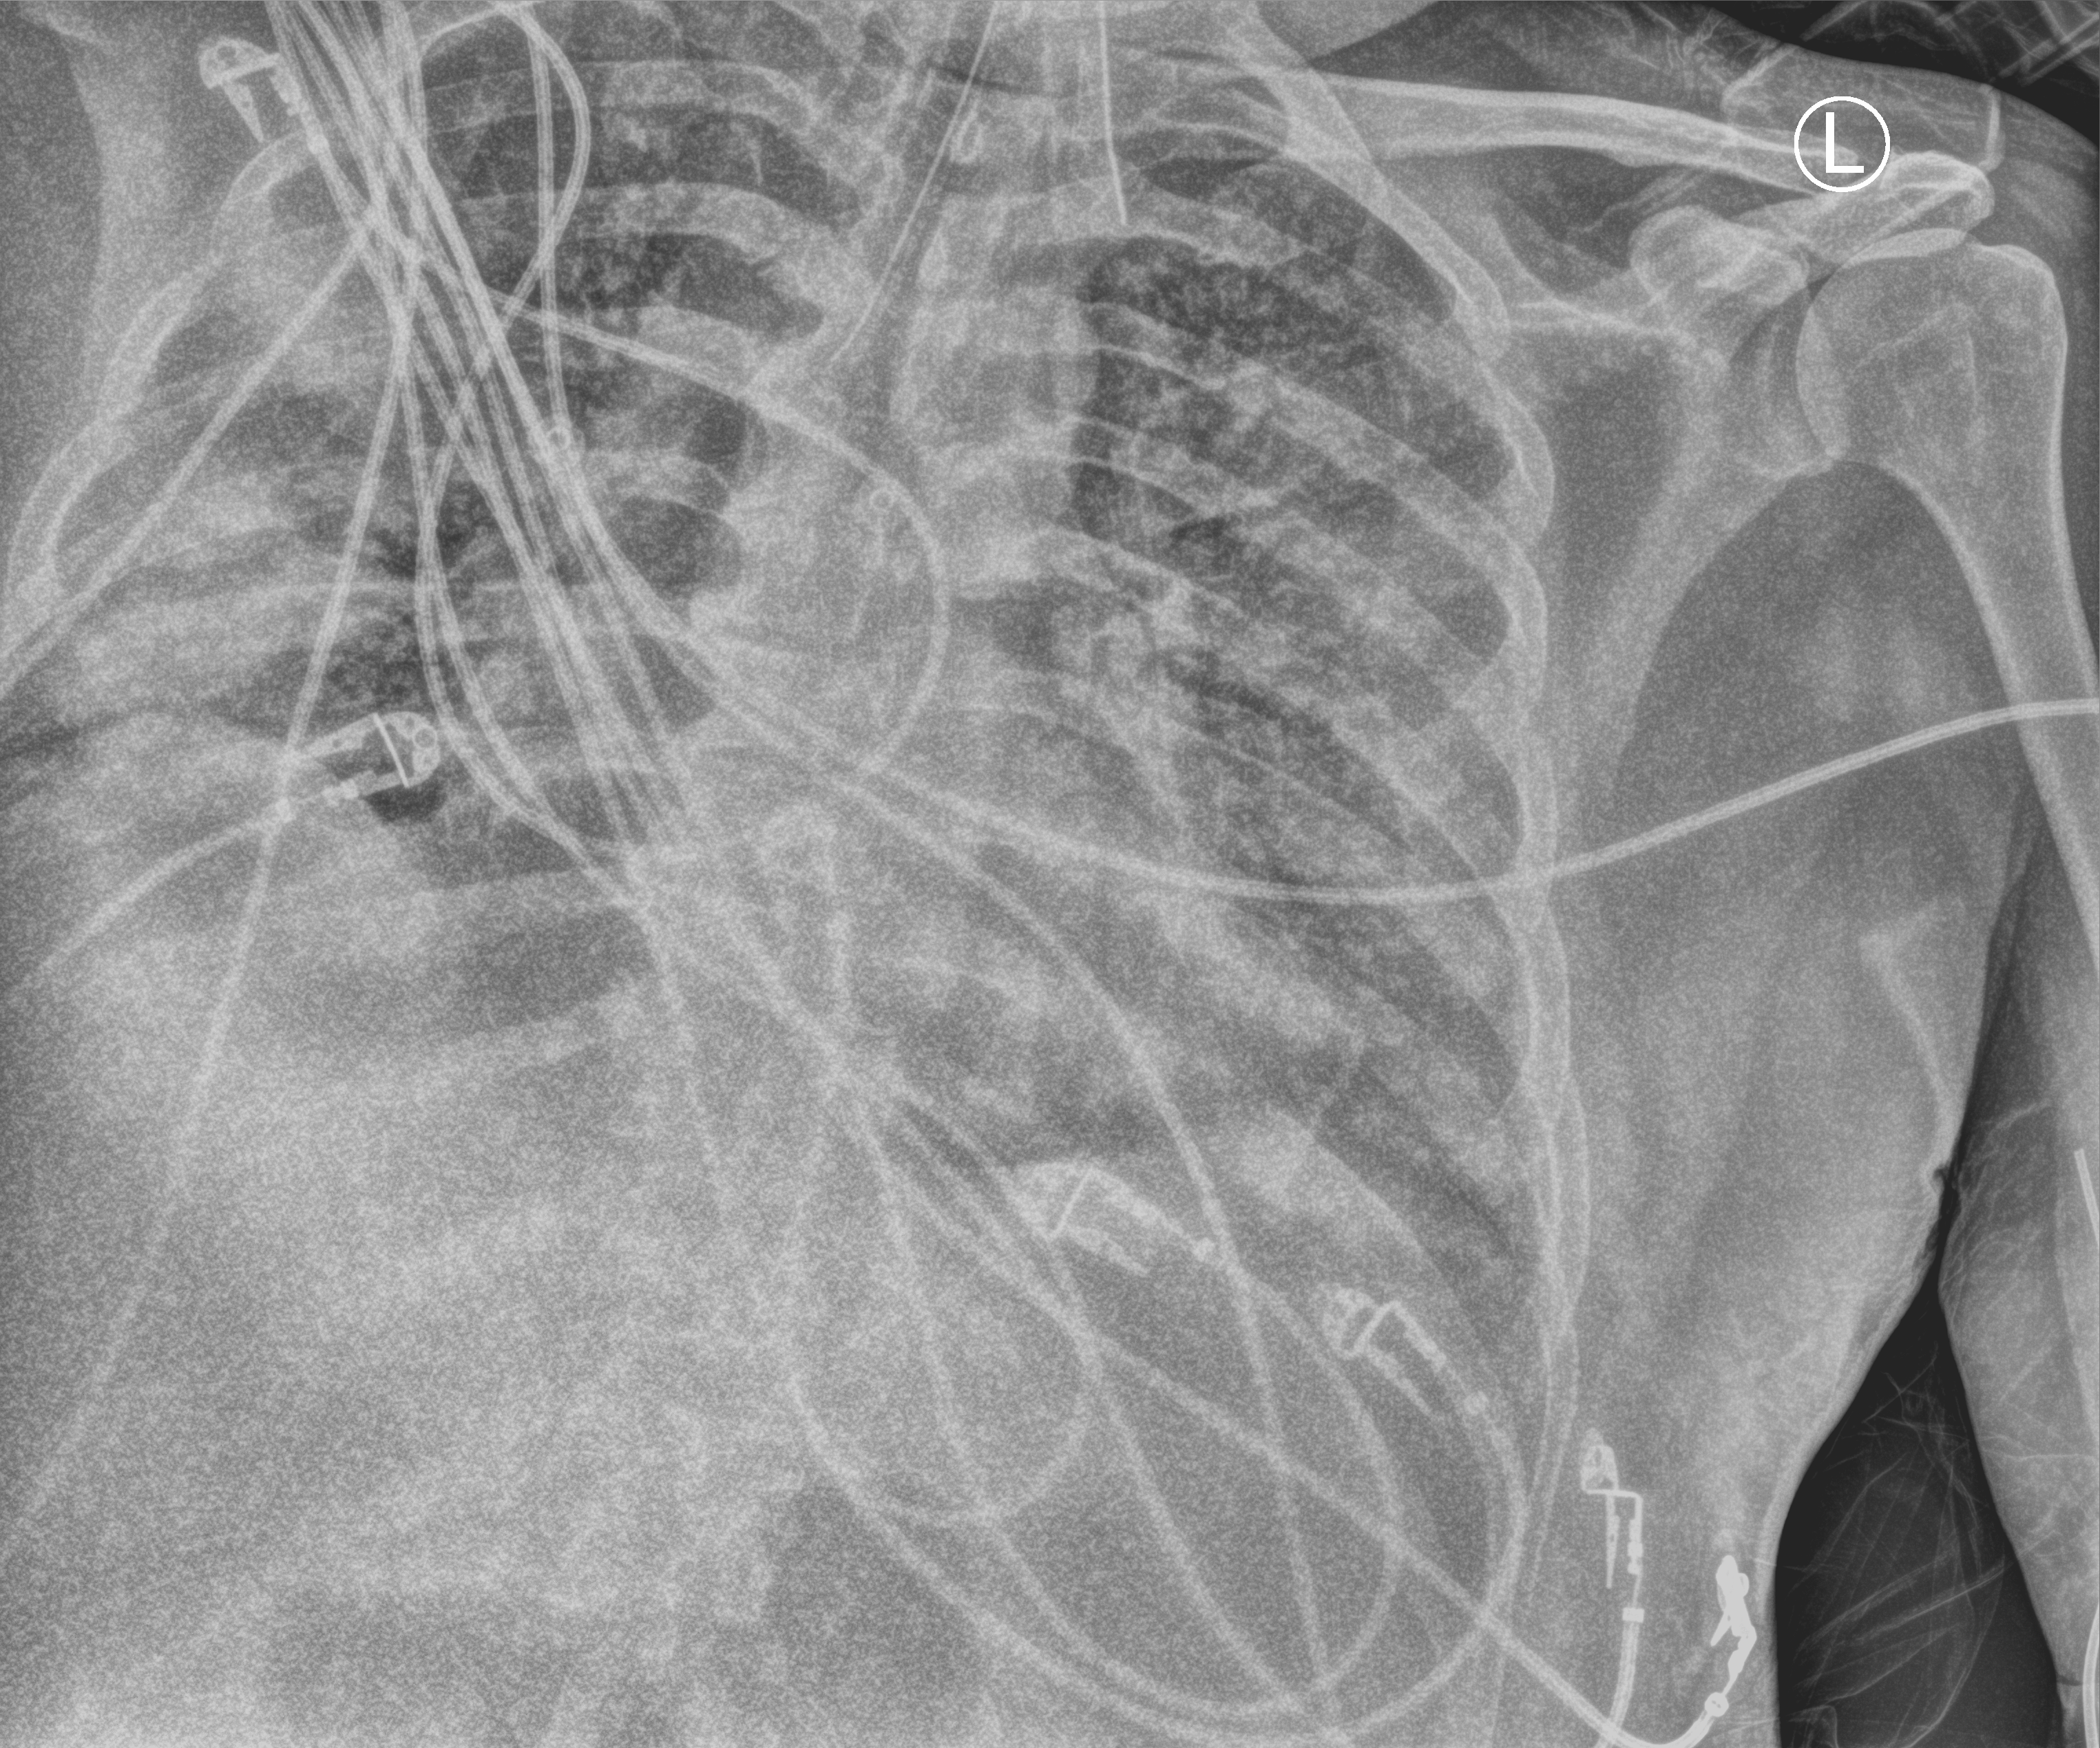
Bedside chest radiograph (computed radiography). Male patient hospitalised with COVID-19, age 18–59 years.
Admission-level facts for this patient (not findings on this image; timing relative to this image not recorded): admitted to intensive care during this hospital stay: yes.